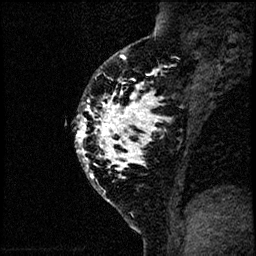
Breast MRI (dynamic contrast-enhanced), one sagittal slice; position 44 of 60 along the scan axis; dynamic contrast-enhanced study with each time point stored as its own series, time point 2 of 4 at this slice position (early post-contrast, ordered by acquisition time); 1.5 T; TE 4.2 ms, TR 17.6 ms; 2 mm slice thickness; 256 × 256 image matrix, field of view 200 × 200 mm. Female patient, age 40 years. Case-level facts recorded for this patient, not image findings: setting: breast cancer imaged before/during neoadjuvant chemotherapy; receptor status: HER2-positive.
Annotated regions visible in this slice (semi-automatic segmentation, software-assisted and operator-edited):
- analysis volume of interest (the breast-tissue region the enhancement analysis was run in; not a lesion): box from (x=69, y=55) to (x=185, y=206) px
- tumour enhancement mask (voxels above the 100 % enhancement threshold inside the analysis volume of interest): (x=74, y=55)–(x=157, y=171)